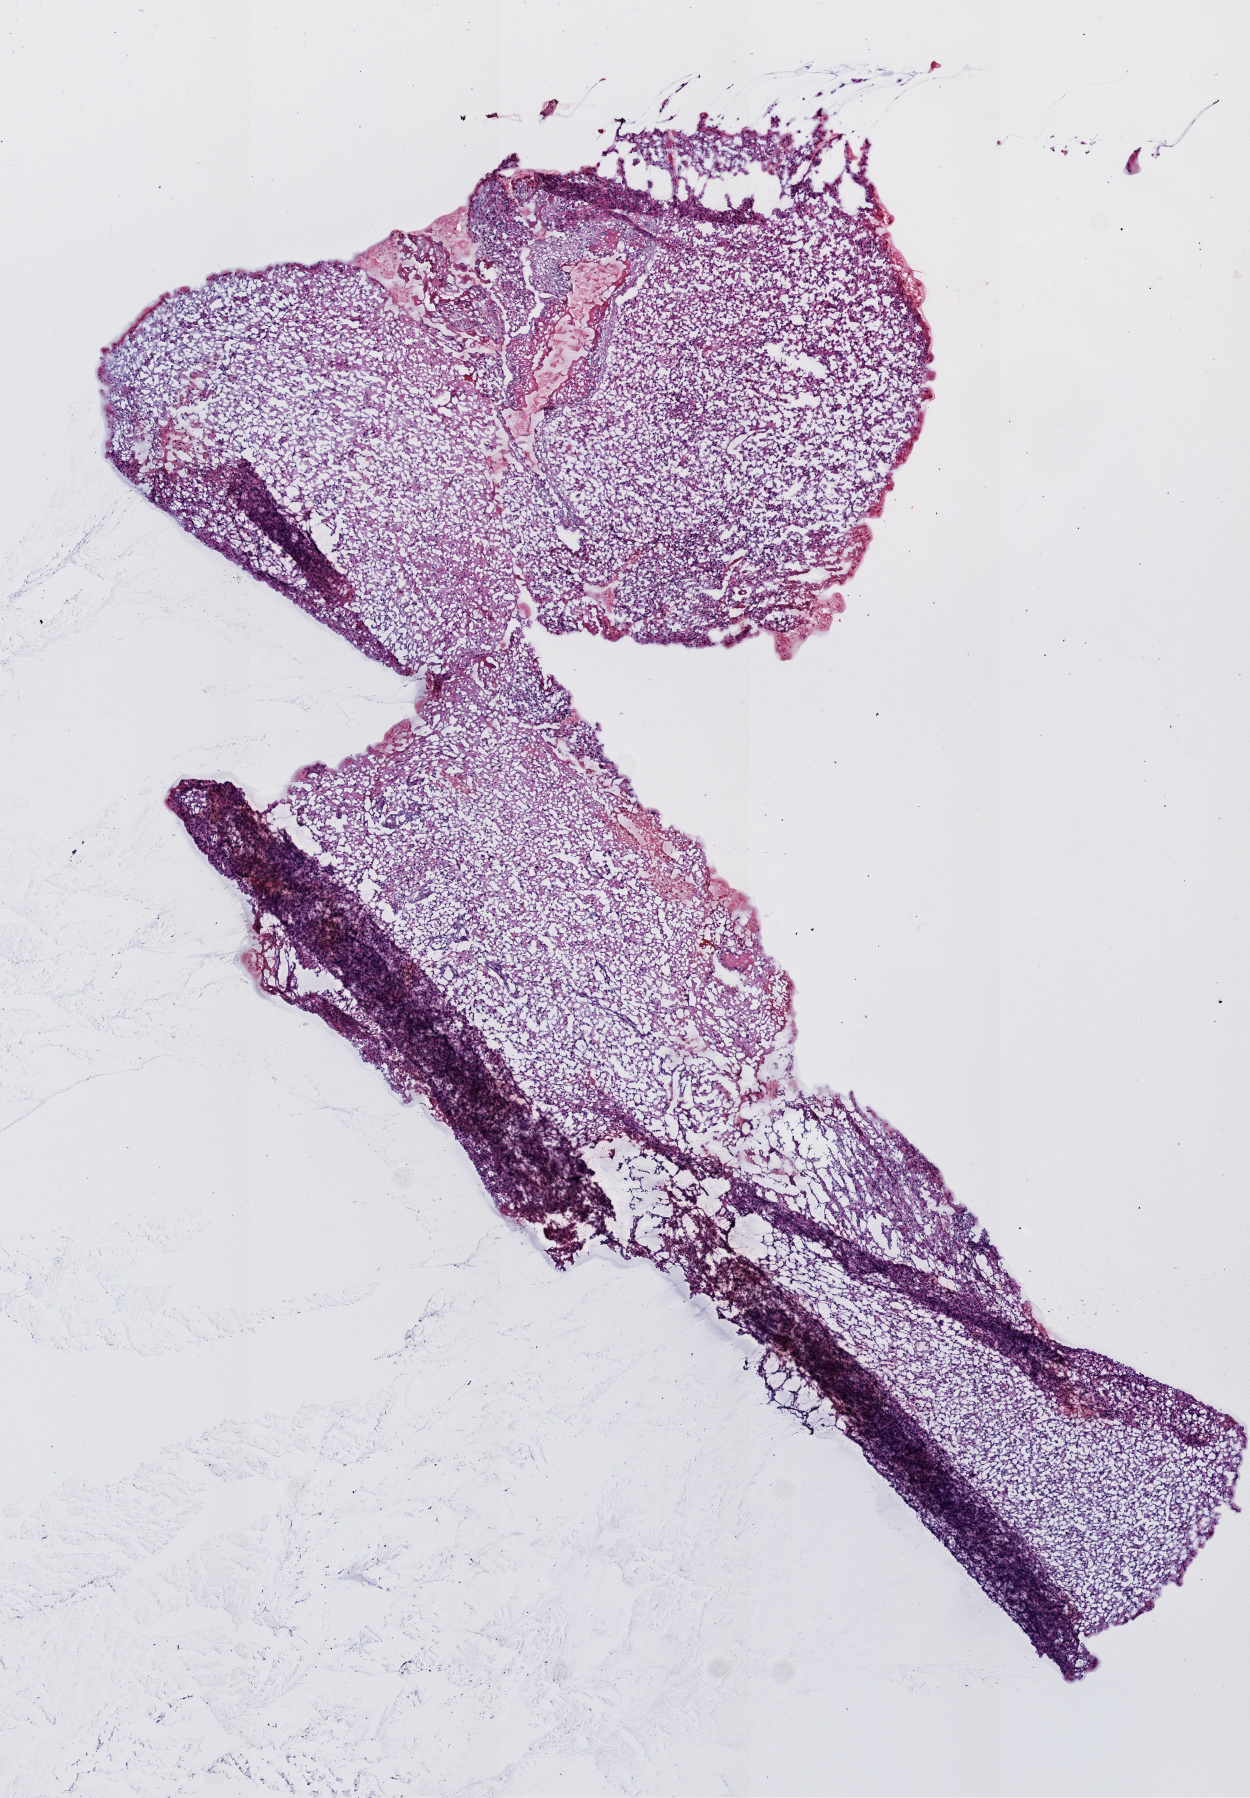
H&E-stained whole-slide image, whole scanned area (about 5.0 x 7.2 mm, slide scanned at 20x) shown as a low-resolution overview. Frozen section. Primary tumour sample from the brain. Female patient; age at initial diagnosis 65 years. Slide review estimates, as recorded: tumour cells 100%, tumour nuclei 70%, normal cells 0%, stromal cells 0%, necrosis 0%.
Diagnosis: Glioblastoma.